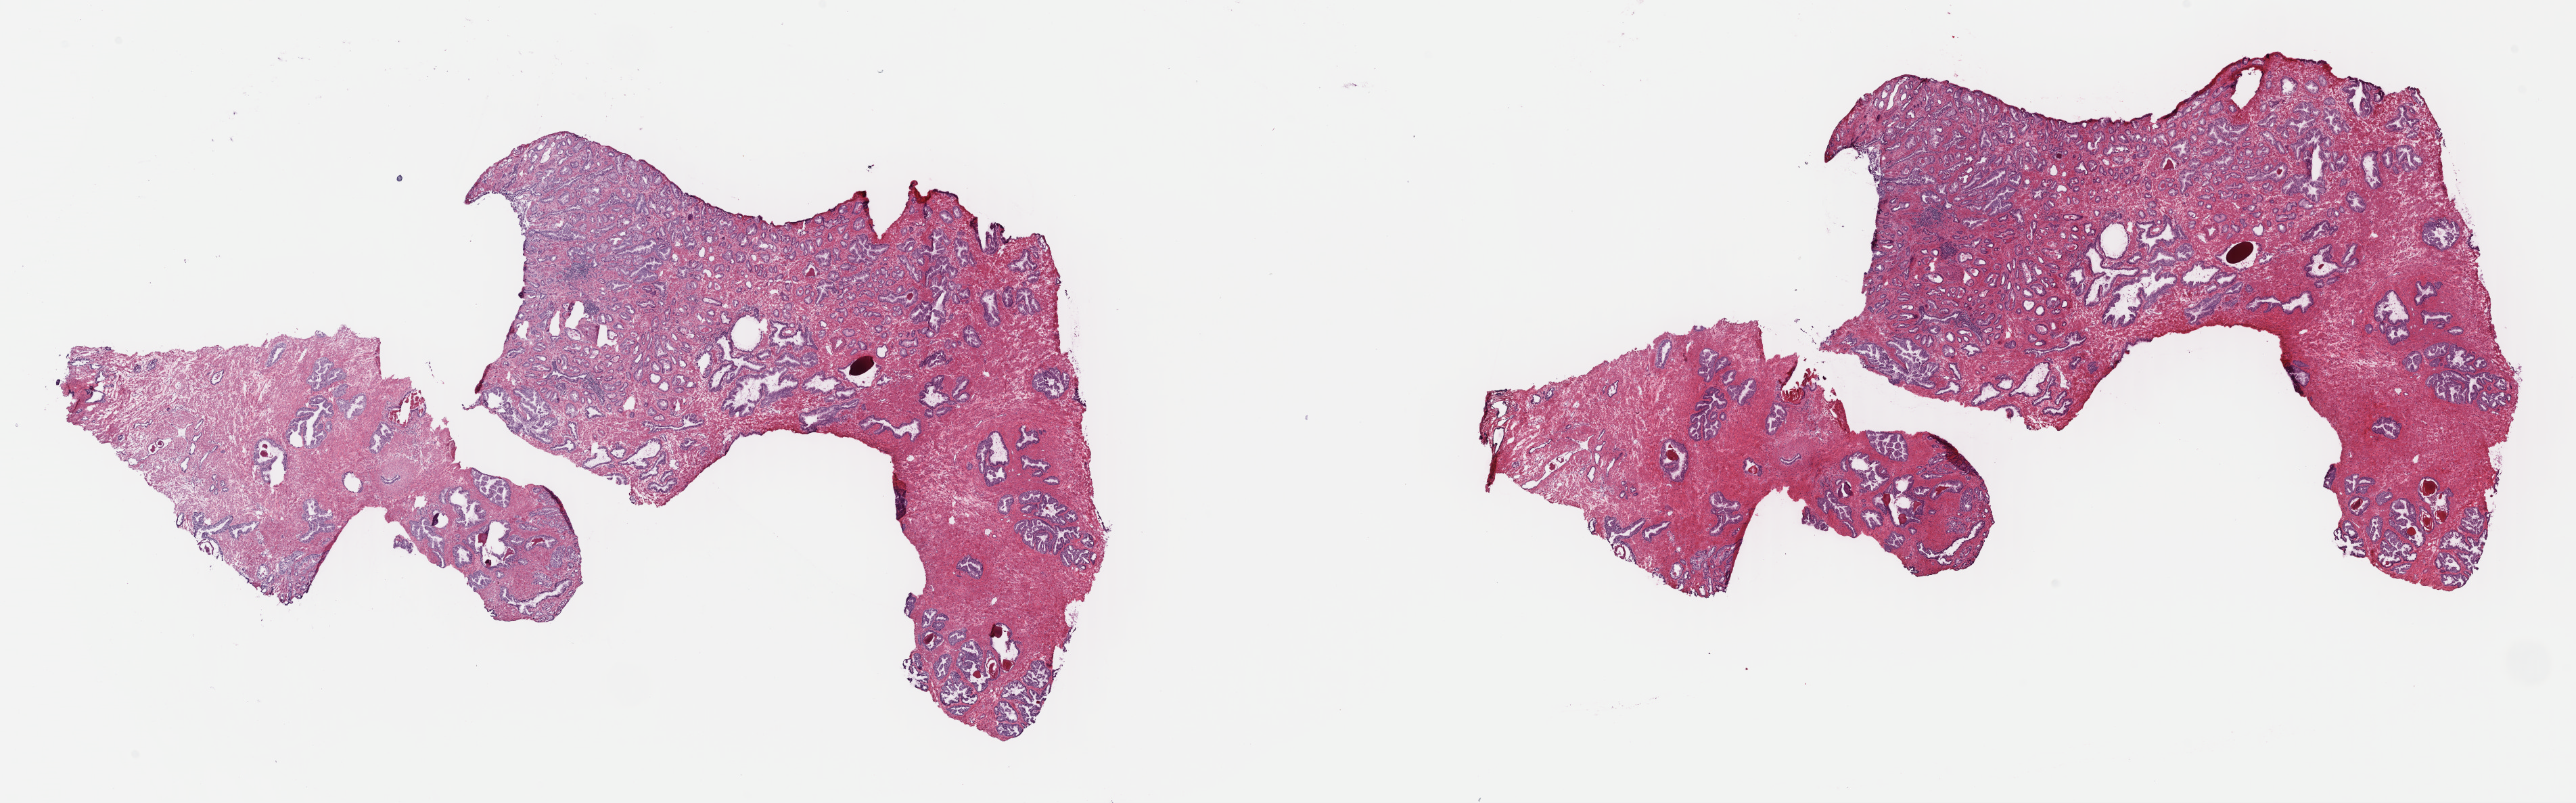
Digitized H&E-stained tissue section (whole slide) — low-resolution overview of the scanned area, about 29.9 x 9.3 mm (slide scanned at 40x), frozen section, sample: primary tumour, prostate. Patient: male, age at initial diagnosis 53 years.
Histologic diagnosis: Adenocarcinoma, NOS (prostate gland).